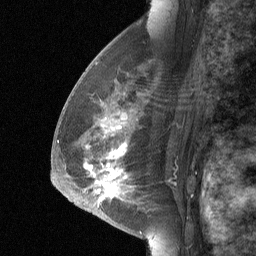
Breast MRI (dynamic contrast-enhanced), one sagittal slice. Slice 38 of 64 in the series (ordered by position). Dynamic contrast-enhanced study with each time point stored as its own series, time point 2 of 3 at this slice position (early post-contrast, ordered by acquisition time). 1.5 T. TE 4.8 ms, TR 27 ms. 2 mm slice thickness. 256 × 256 image matrix. Patient: female, 56 years. From the clinical record (not read from this slice): setting: breast cancer imaged before/during neoadjuvant chemotherapy; receptor status: HER2-positive.
Annotated regions visible in this slice (semi-automatic segmentation, software-assisted and operator-edited):
- analysis volume of interest (the breast-tissue region the enhancement analysis was run in; not a lesion): bounding box [x1, y1, x2, y2] px = [68, 83, 158, 214]
- tumour enhancement mask (voxels above the 90 % enhancement threshold inside the analysis volume of interest): [95, 126, 126, 202]